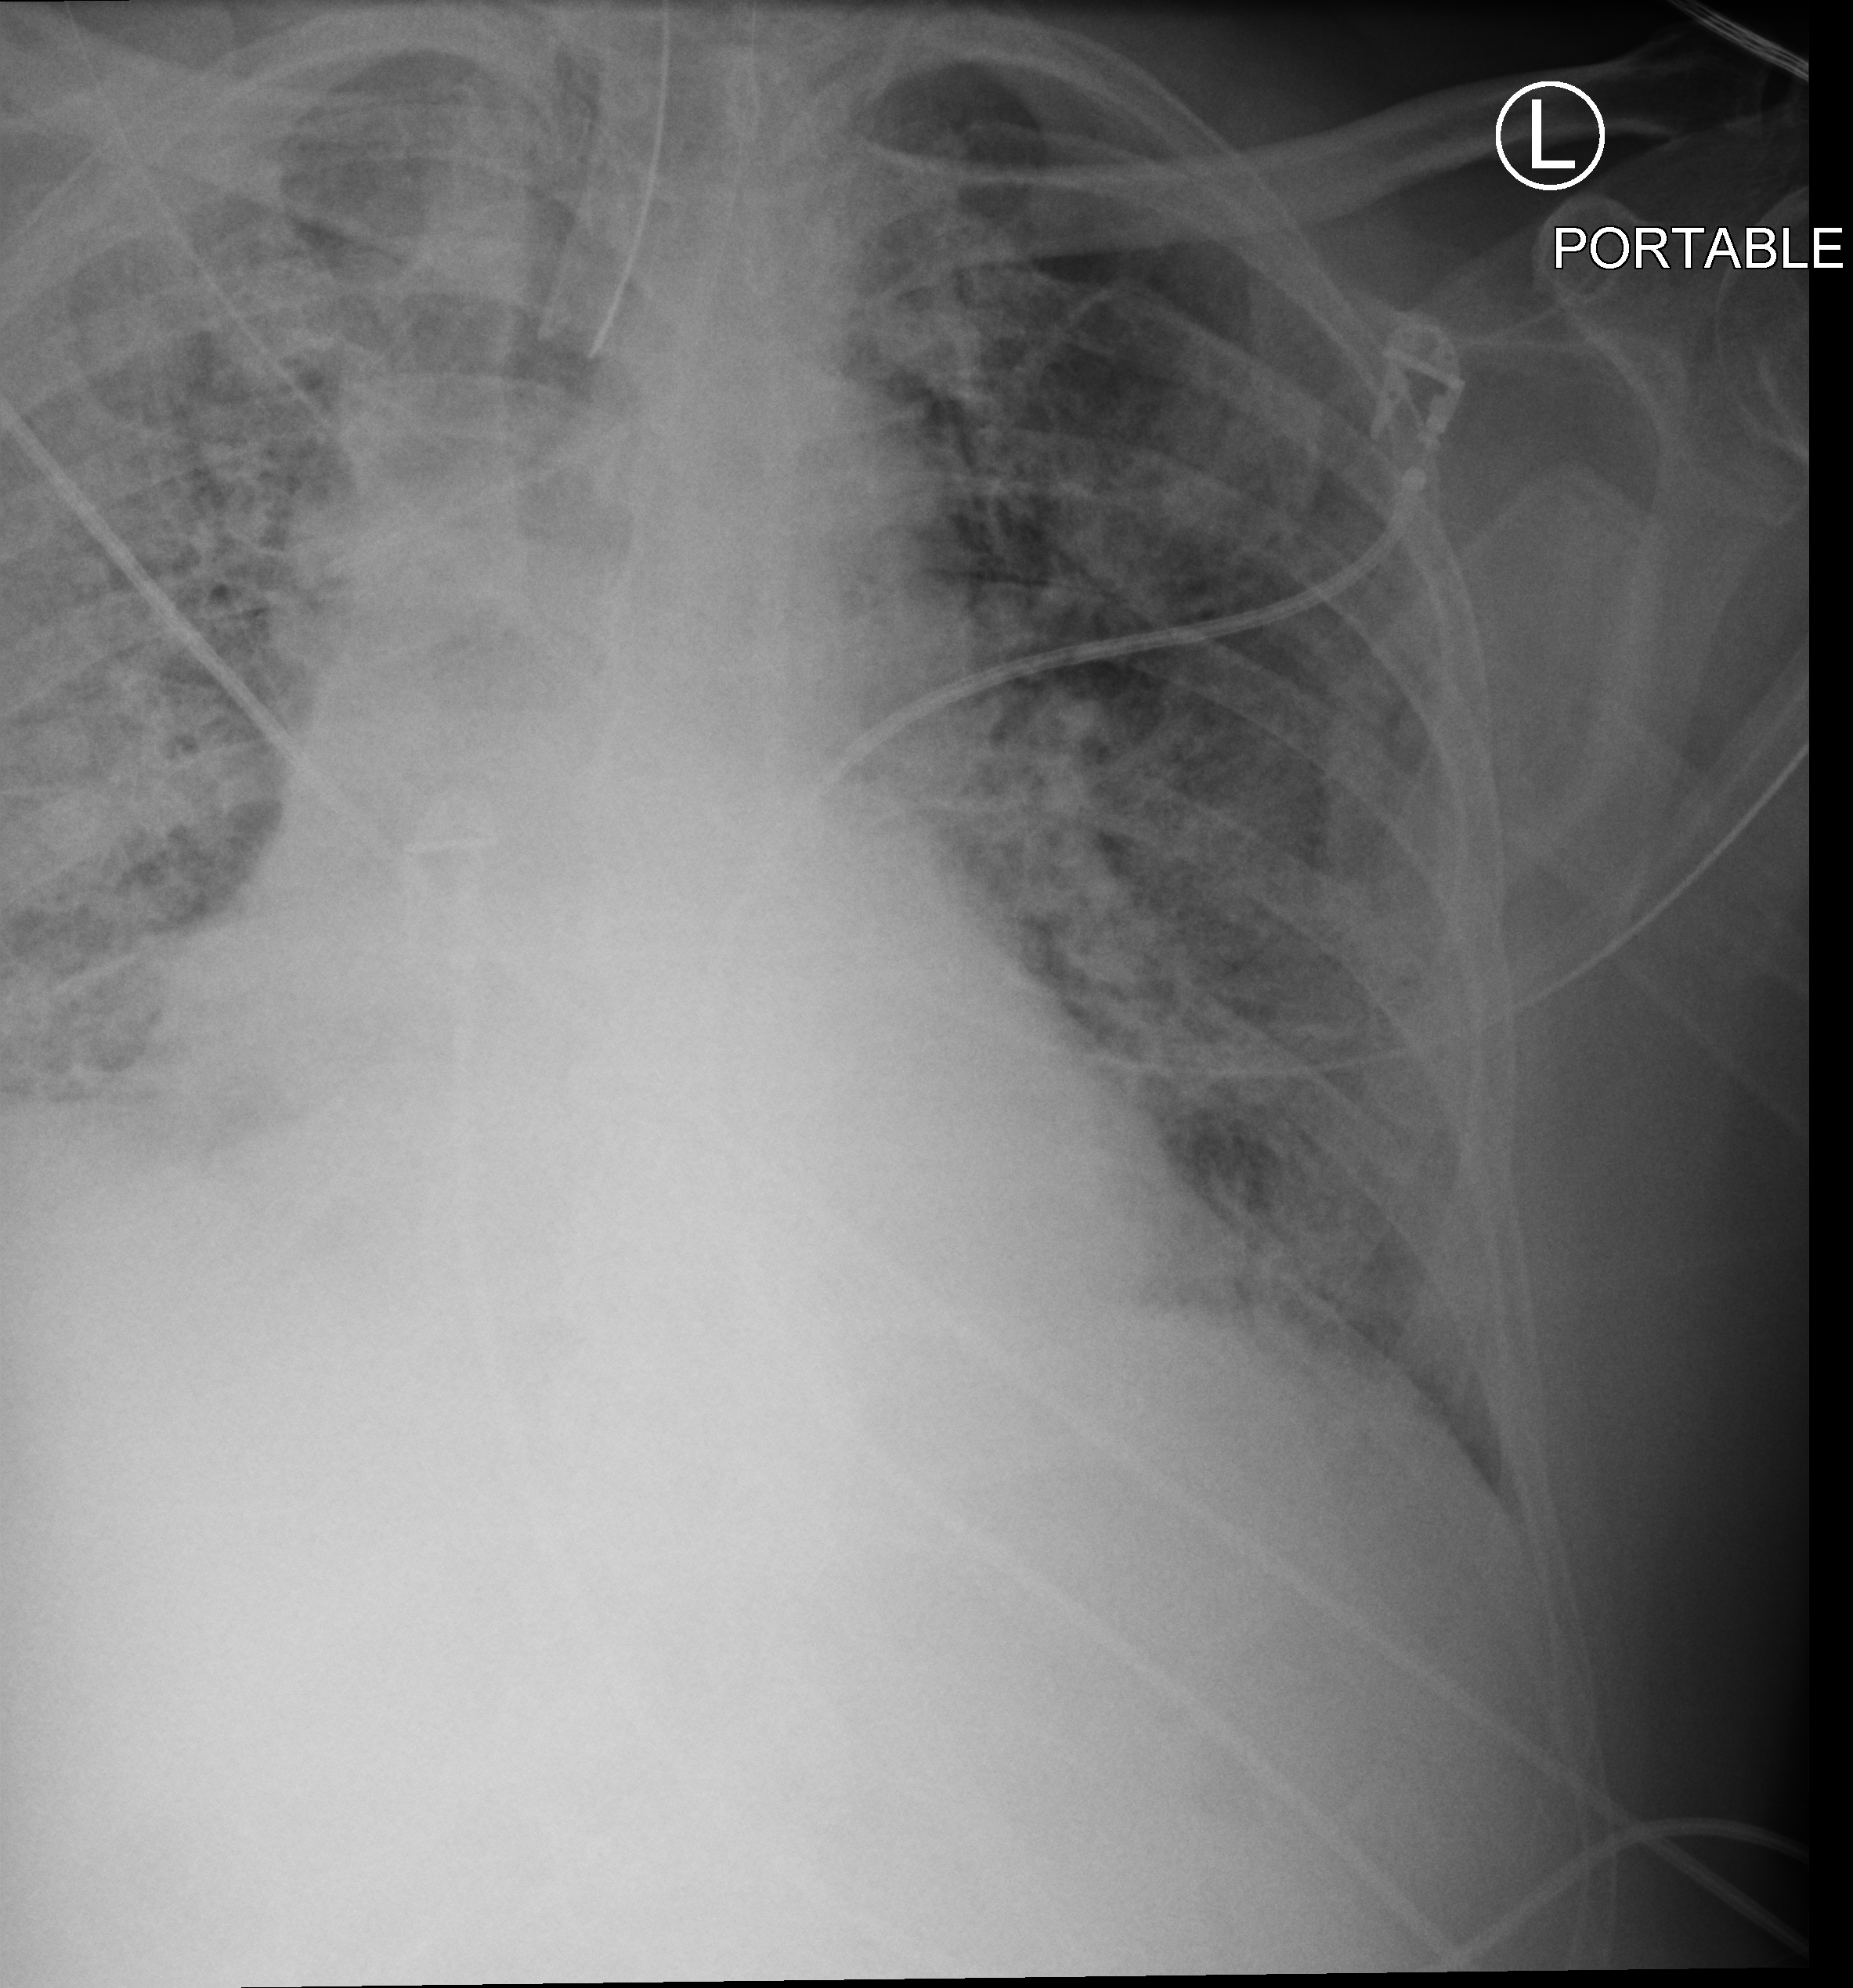
Bedside chest radiograph (computed radiography); anteroposterior (AP) projection. Patient hospitalised with COVID-19; male, aged 75–90 years.
Admission-level facts for this patient (not findings on this image; timing relative to this image not recorded):
- mechanically ventilated during this hospital stay: yes